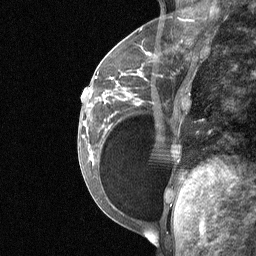
Breast MRI (dynamic contrast-enhanced), one sagittal slice. Position 23 of 64 along the scan axis. Dynamic contrast-enhanced study with each time point stored as its own series, time point 2 of 3 at this slice position (early post-contrast, ordered by acquisition time). 1.5 T. TE 4.8 ms, TR 27 ms. 2 mm slice thickness. 256 × 256 image matrix. Female patient, age 34 years. Case-level facts recorded for this patient, not image findings: setting: breast cancer imaged before/during neoadjuvant chemotherapy; receptor status: HR-positive, HER2-negative.
Annotated regions visible in this slice (semi-automatic segmentation, software-assisted and operator-edited):
- analysis volume of interest (the breast-tissue region the enhancement analysis was run in; not a lesion): box from (x=92, y=50) to (x=188, y=185) px
- tumour enhancement mask (voxels above the 90 % enhancement threshold inside the analysis volume of interest): (x=96, y=77)–(x=105, y=97)